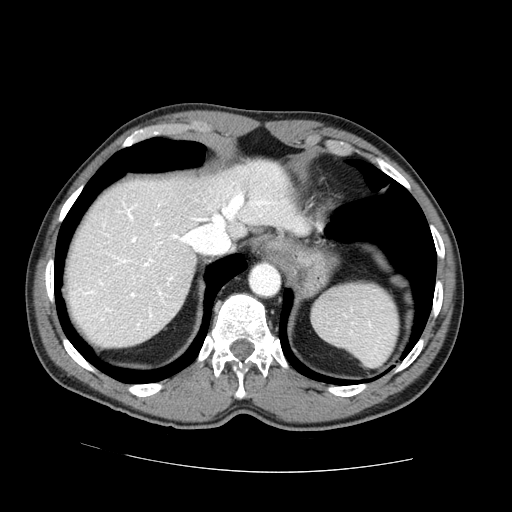
Contrast-enhanced abdominal CT (liver protocol), one axial slice; slice 59 of 73 in the series (ordered by position); 100 kVp; one of 2 acquisitions stored at this slice position; soft-tissue window (W 400 / L 40 HU); 2.5 mm slice thickness; 512 × 512 image matrix. Case-level facts recorded for this patient, not image findings: diagnosis: hepatocellular carcinoma (patient treated with transarterial chemoembolisation; whether this scan precedes or follows treatment is not stated here); TNM stage (as recorded): Stage-IVA; Child-Pugh class: A; tumour differentiation: no biopsy; tumour nodularity: uninodular.
Annotated regions visible in this slice (semi-automatic segmentation, software-assisted and operator-edited):
- abdominal aorta: bounding box [x1, y1, x2, y2] px = [251, 263, 280, 296]
- liver parenchyma outside the tumour (the mass and vessels are separate outlines, so this box may not span the whole liver): [66, 160, 310, 346]
- liver vessels: [84, 193, 269, 320]